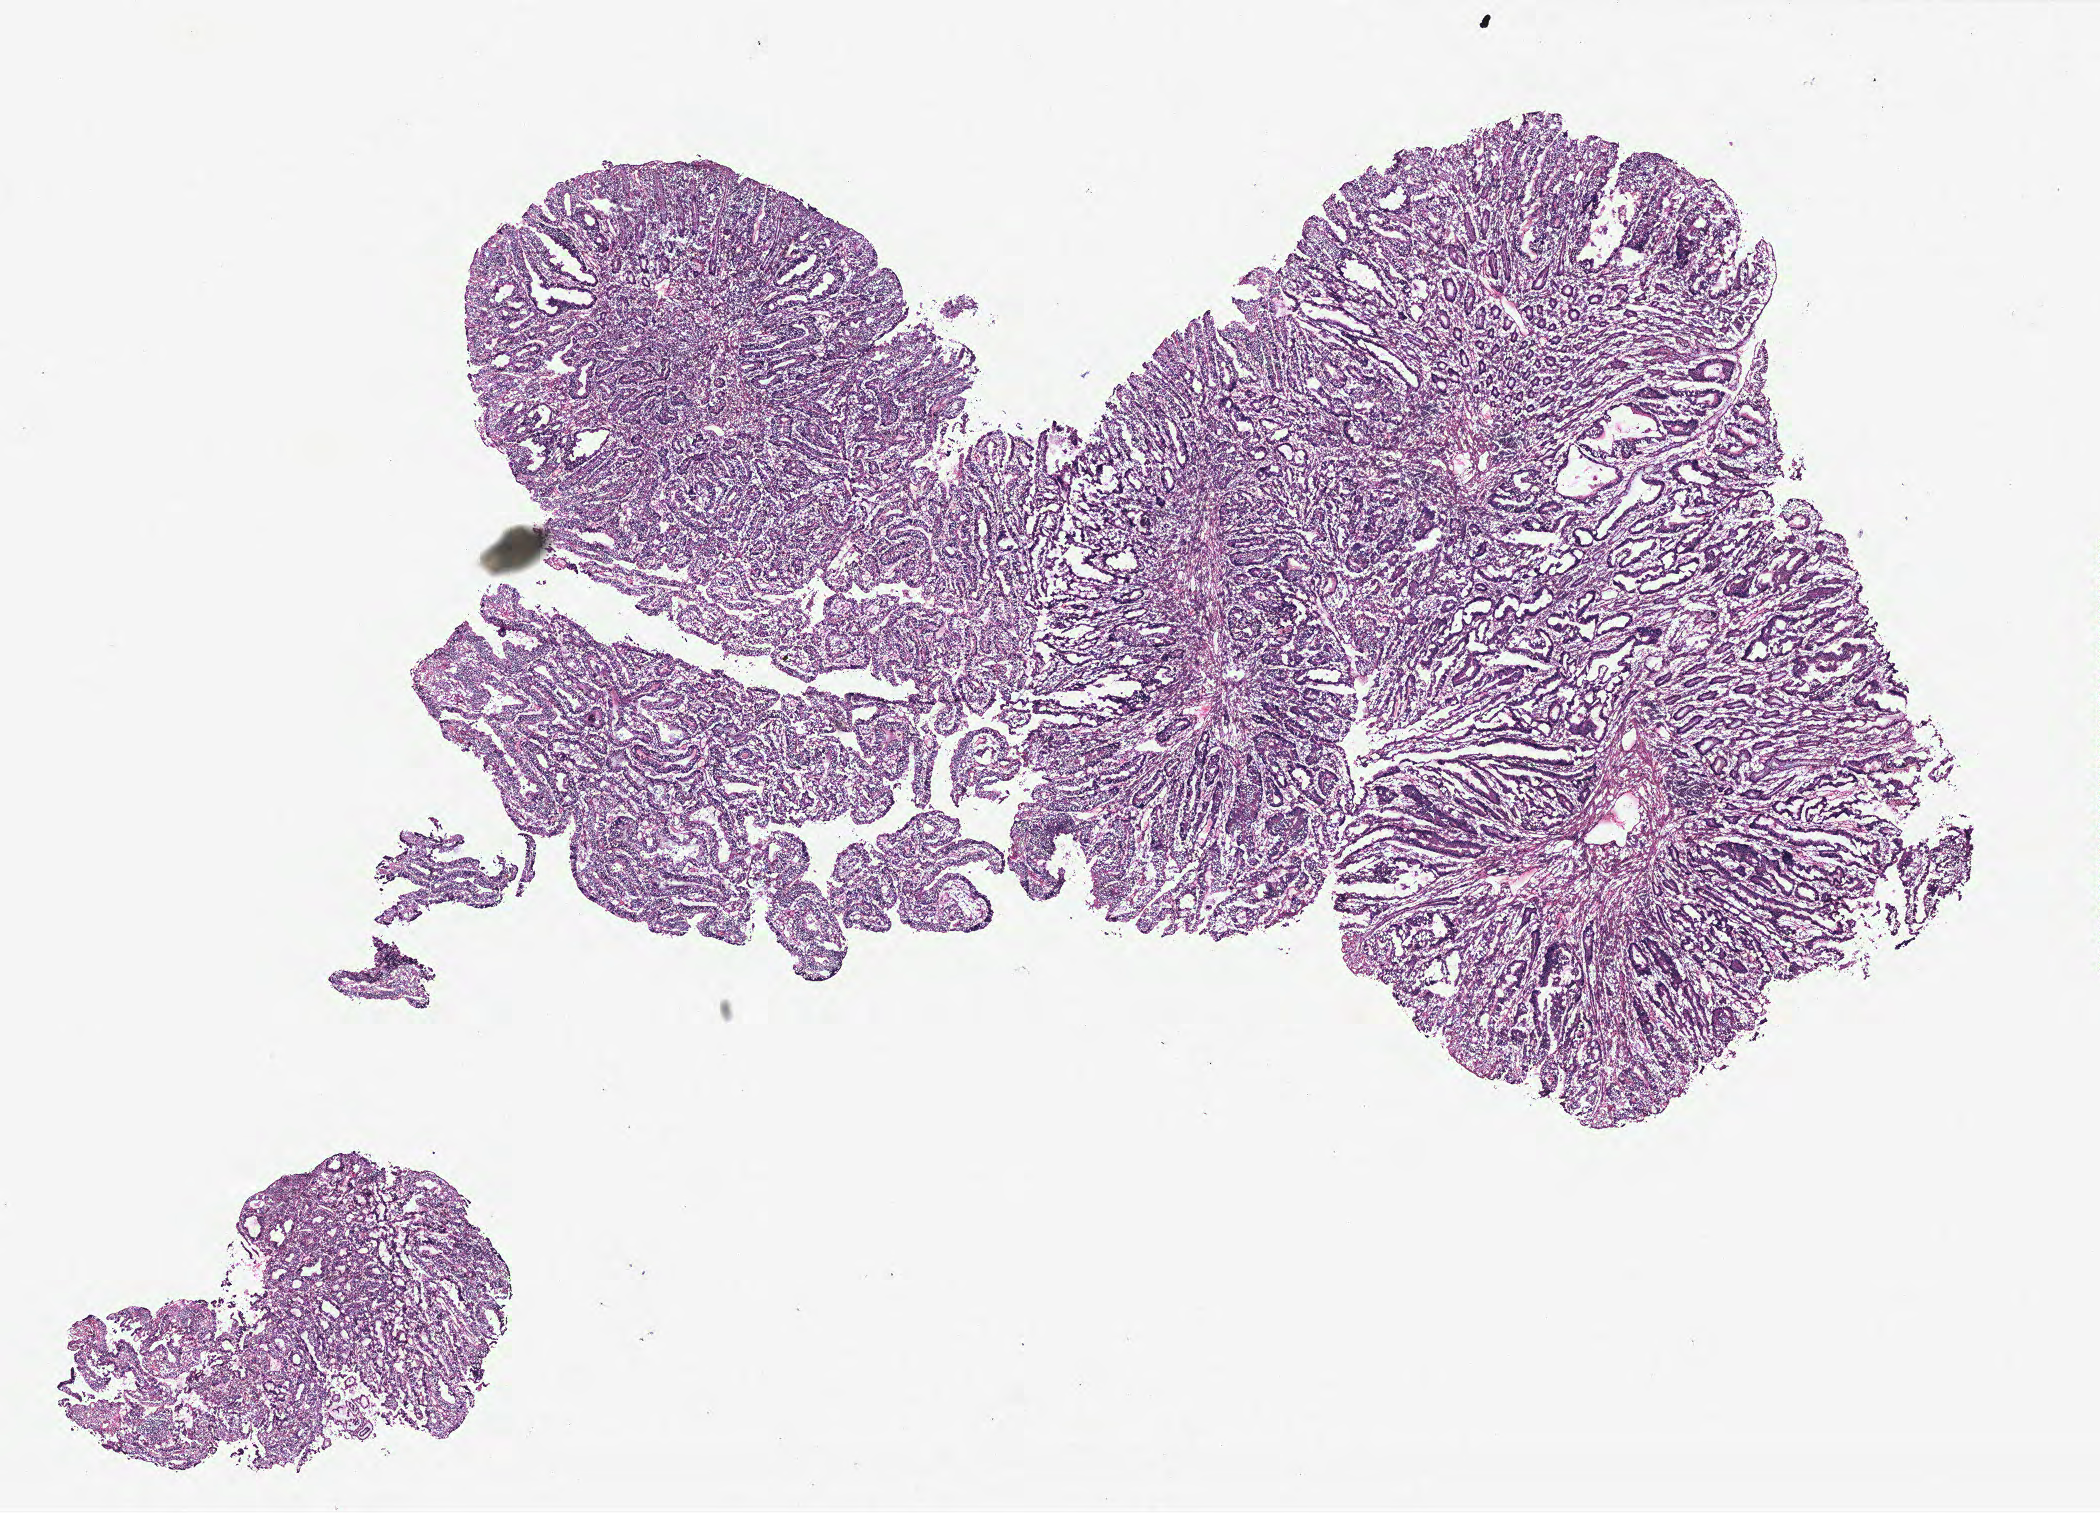
Hematoxylin and eosin (H&E) stained whole-slide image, whole scanned area (about 16.8 x 12.1 mm, acquisition: 40x scan) shown as a low-resolution overview. Colon, tissue type not recorded.
Patient diagnosis (cohort enrolment): colon cancer (colon).